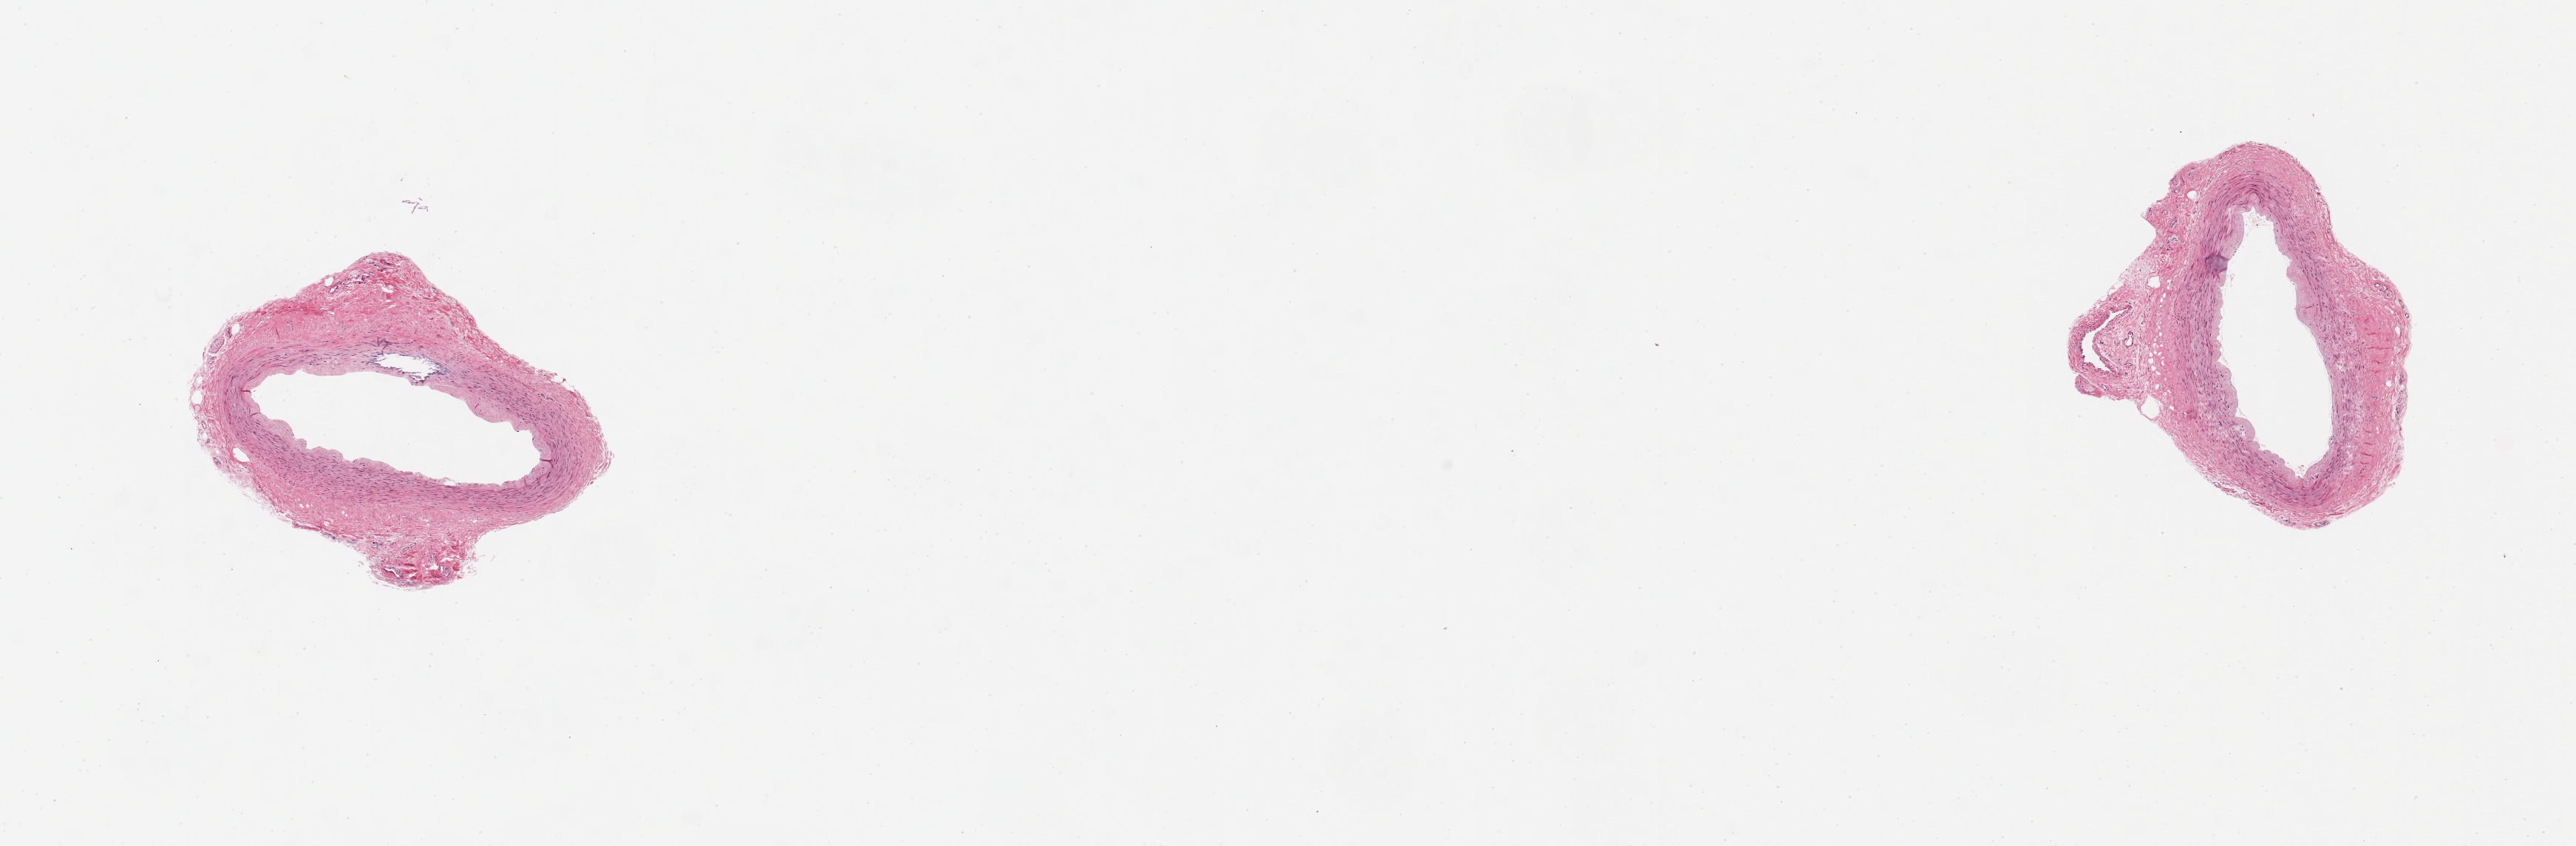
Whole-slide image, H&E stain — whole scanned area (about 13.8 x 4.5 mm) shown as a low-resolution overview, PAXgene-fixed, paraffin-embedded tissue, section of tibial artery (target tissue), donor tissue sample.
Pathologist's review note for this sample: 2 pieces 2x1.5 mm each; small vein at edge of one.